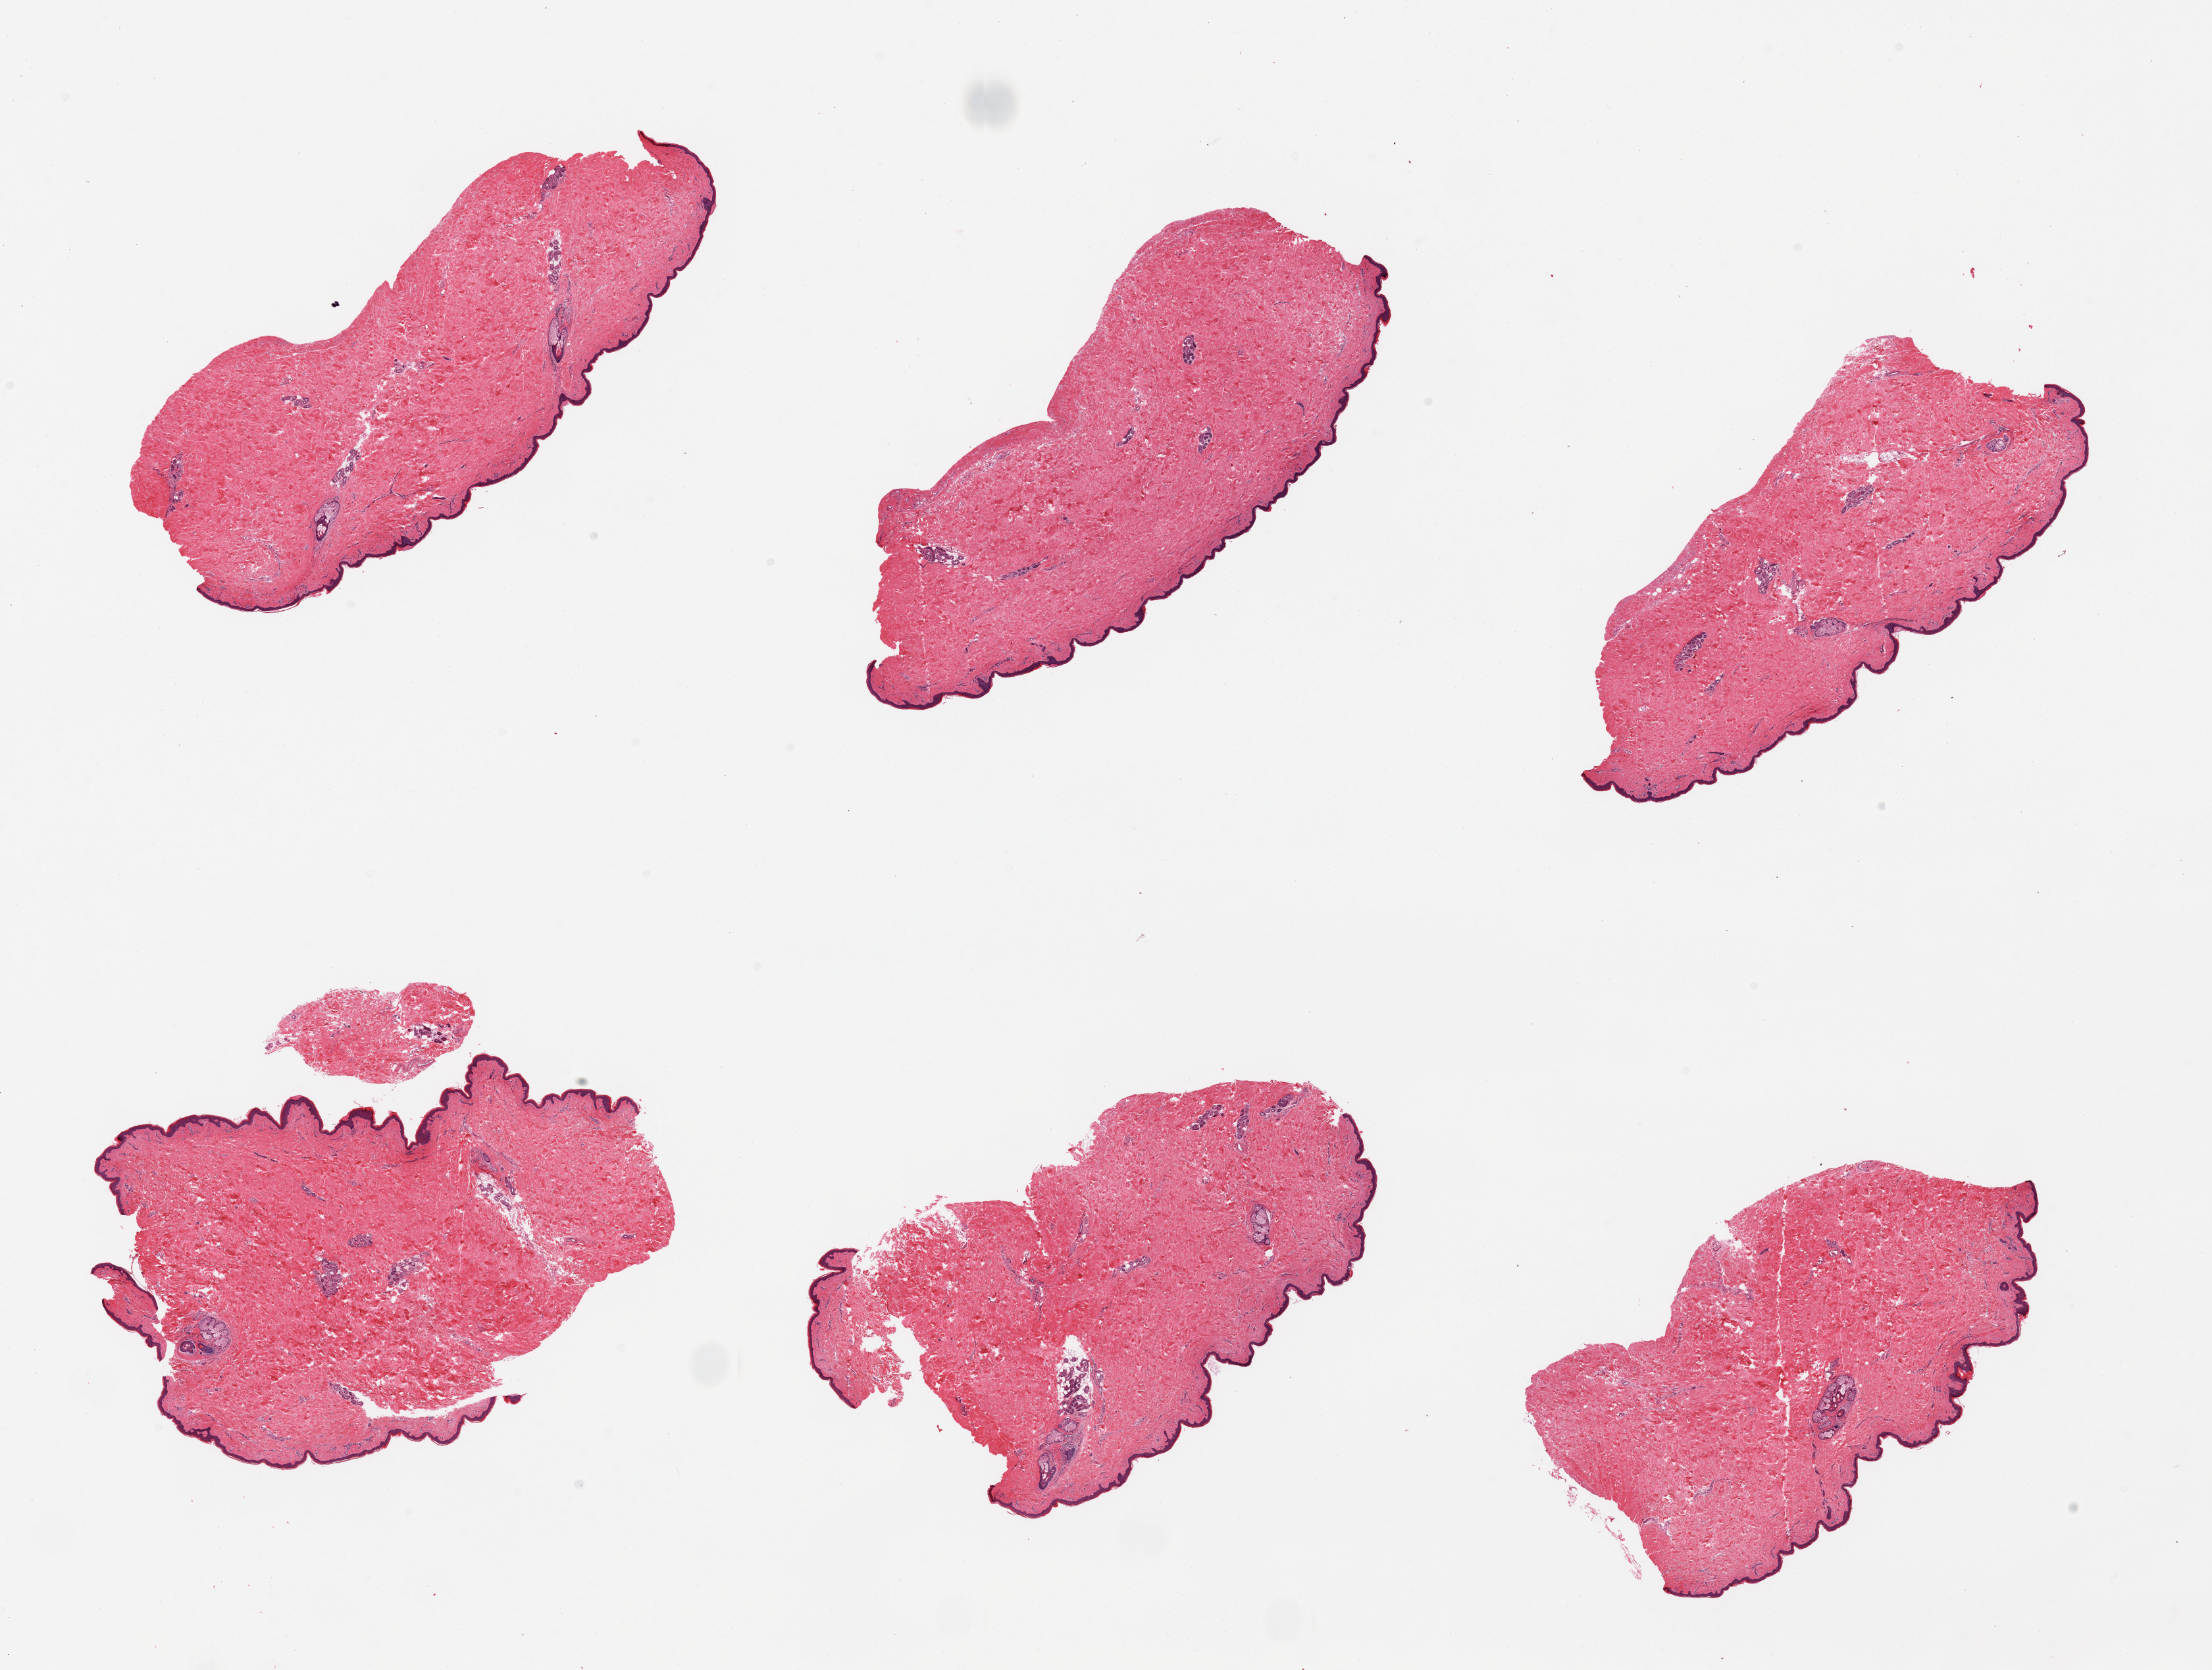
Haematoxylin and eosin whole-slide image, a low-resolution overview of the entire scanned area, about 26.6 x 20.1 mm. PAXgene-fixed paraffin-embedded (PFPE) section. Target tissue: skin of suprapubic region. Tissue donor sample. Donor: female.
Pathologist's review note for this sample: 6 pieces; well trimmed.